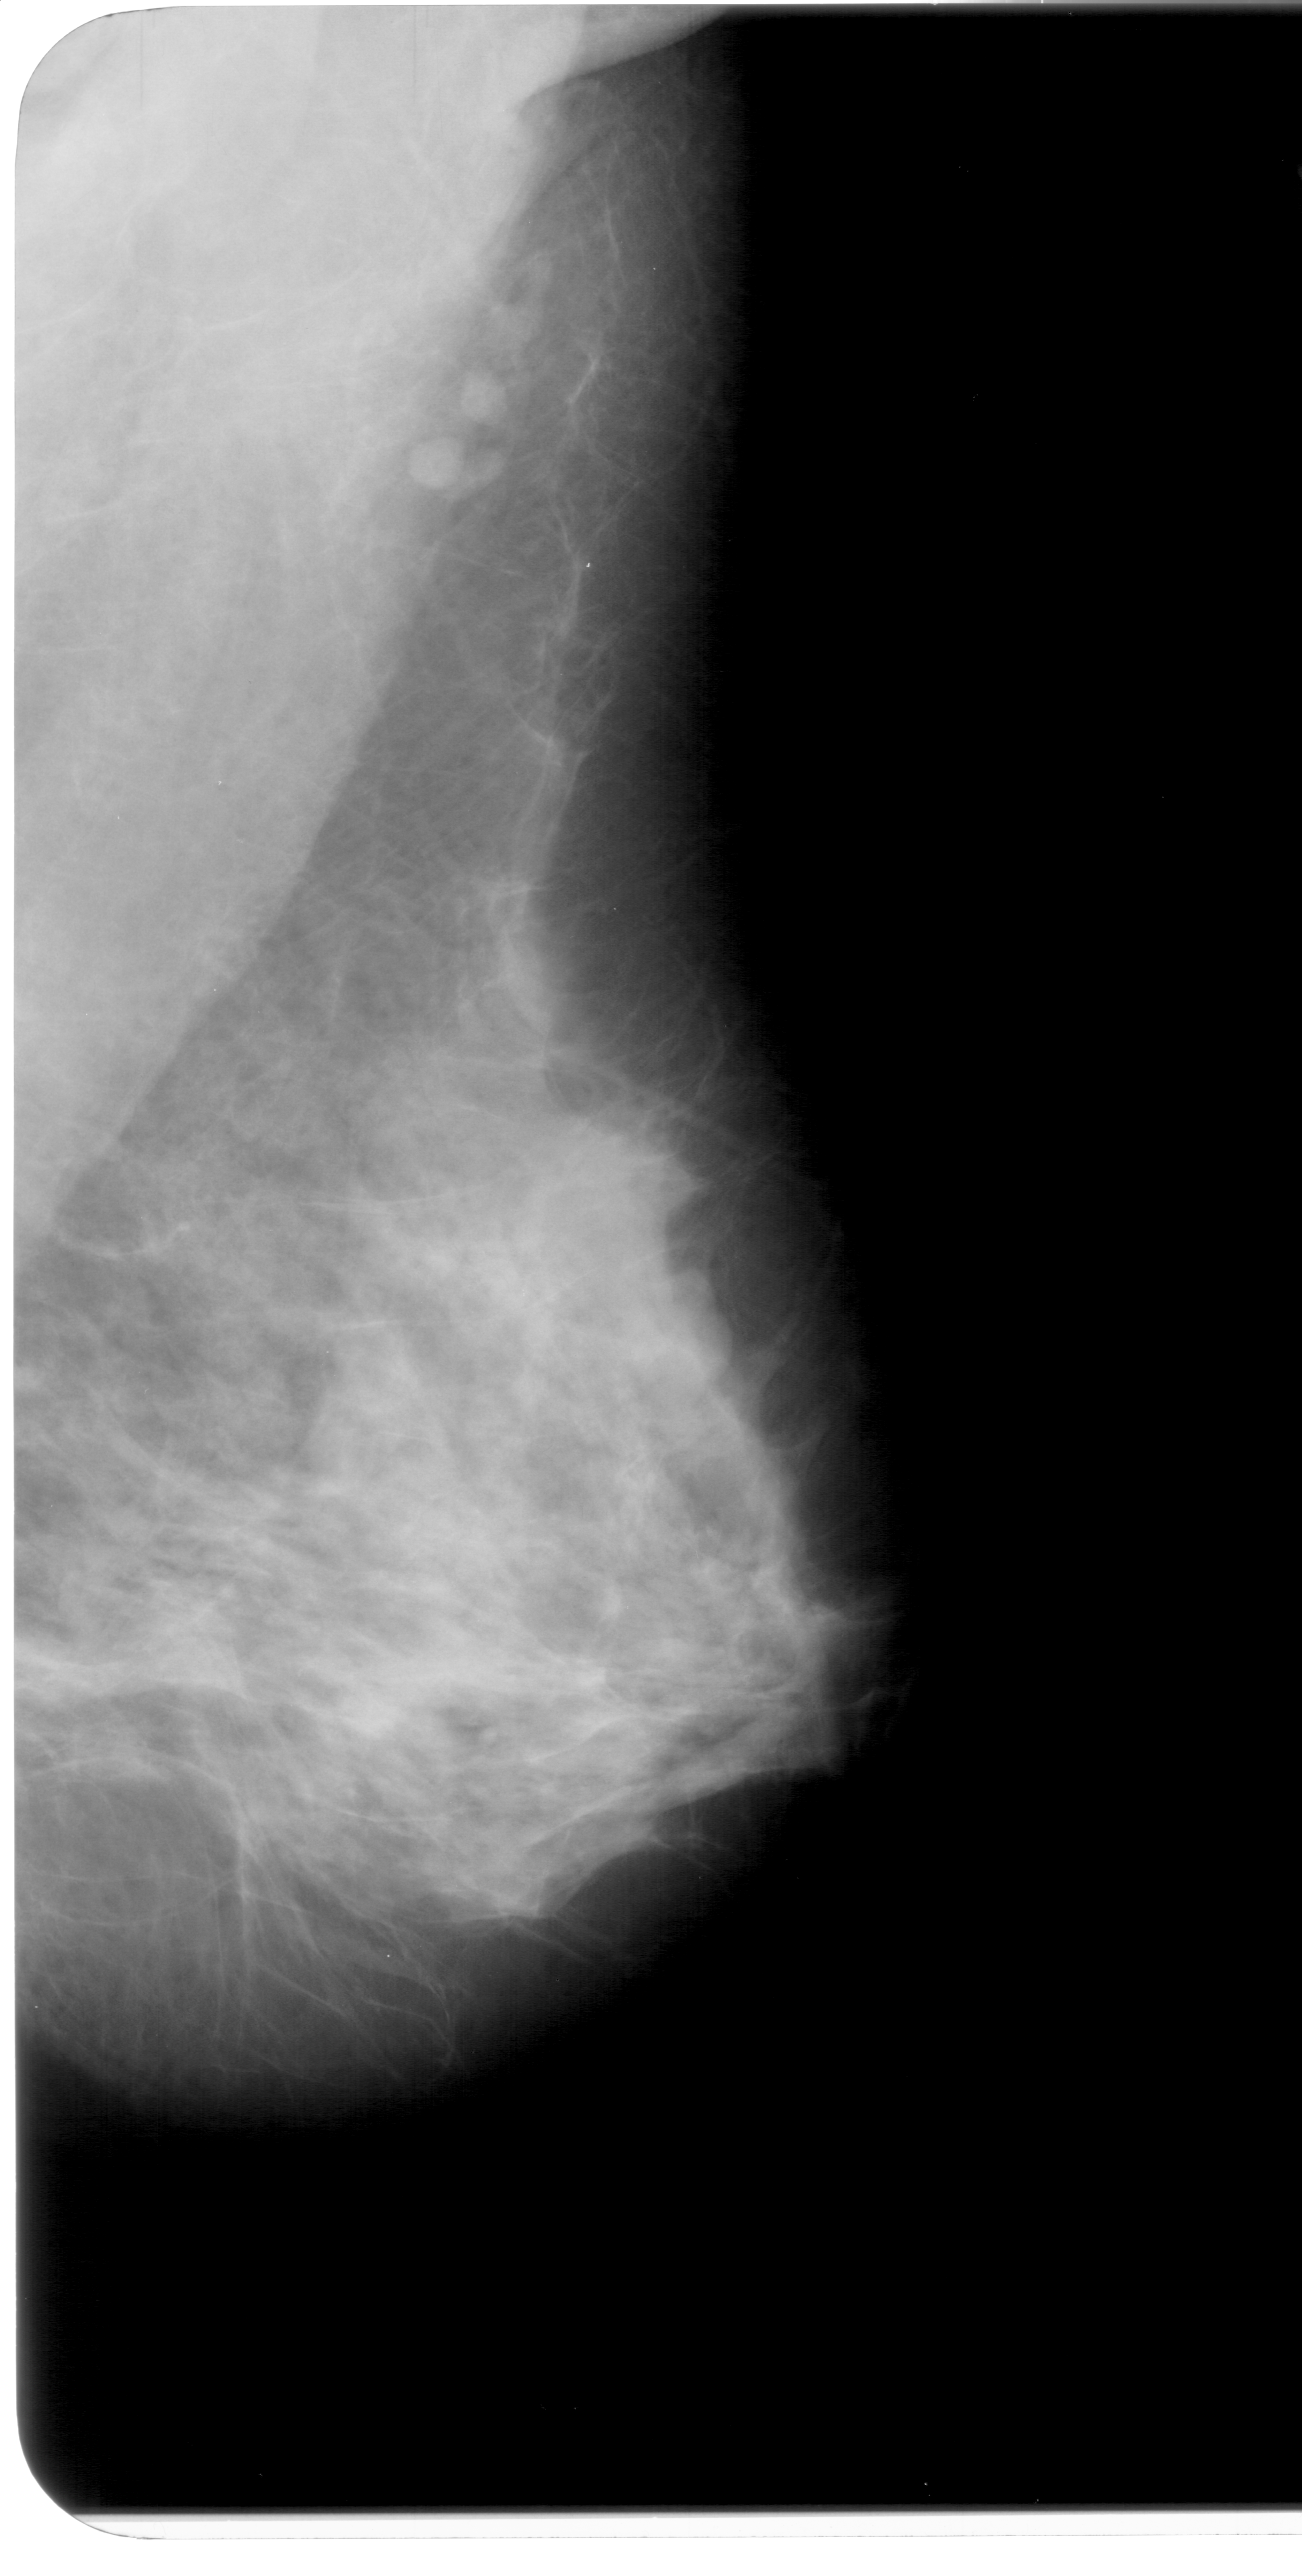
Scanned film-screen mammogram. Right breast. Mediolateral oblique (MLO) view. Breast composition: heterogeneously dense (BI-RADS density category 3 of 4). 1302 × 2576 image matrix.
Expert-marked regions of interest on this image (one box per marked abnormality):
- mass, shape lobulated, margins obscured; BI-RADS assessment category 4; subtlety rating 2 on a 1 (subtle) to 5 (obvious) scale; pathology result (as recorded, not read from the image): benign: bounding box [x1, y1, x2, y2] px = [605, 1296, 732, 1400]